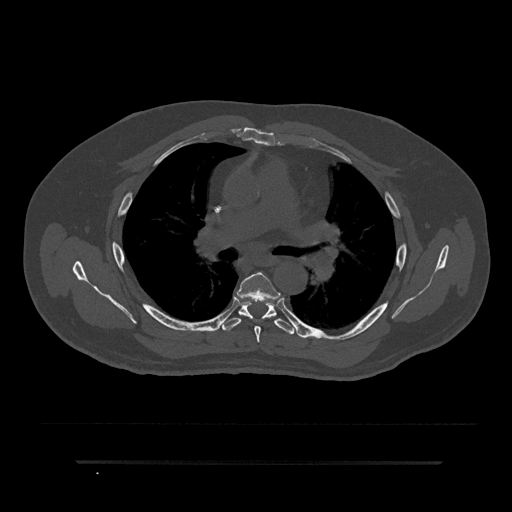
CT including the spine, one axial slice; position 552 of 797 along the scan axis; reconstruction kernel Br40s/3; bone window (W 1800 / L 400 HU); 0.5 mm slice thickness; 512 × 512 image matrix, field of view 464 × 464 mm. Patient: male, 59 years. Case-level facts recorded for this patient, not image findings: primary cancer: bile ducts; vertebrae with lytic lesions (as recorded): T10.
Annotated regions visible in this slice (semi-automatically segmented with operator editing):
- T5 vertebra: box from (x=236, y=272) to (x=278, y=343) px
- T6 vertebra: (x=222, y=299)–(x=294, y=335)